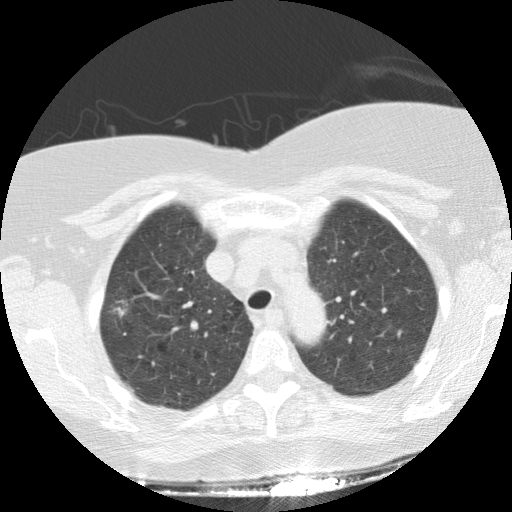
Chest CT (low-dose screening protocol), one axial image, first (baseline) screen, lung window (W 1500 / L -600 HU), 120 kVp, slice 29 of 136 in the series, 512 × 512 image matrix. Female, age 64 years at enrolment. Current smoker at enrolment.
Expert reader's lesion annotation, bounding box [x1, y1, x2, y2] px = [89, 271, 143, 334]. Screening reader's record for this exam (one nodule recorded; not confirmed to be the boxed lesion): non-calcified nodule or mass ≥4 mm, right upper lobe, 17 × 16 mm, spiculated (stellate) margins, soft tissue attenuation. Official screen result: positive, change unspecified: nodule(s) >= 4 mm or enlarging nodule(s), mass(es), or other non-specific abnormalities suspicious for lung cancer. Later outcome: lung cancer diagnosed 70 days after this screen — adenocarcinoma, NOS, right upper lobe, stage IIIA (AJCC 6th edition), 15 mm at pathology.